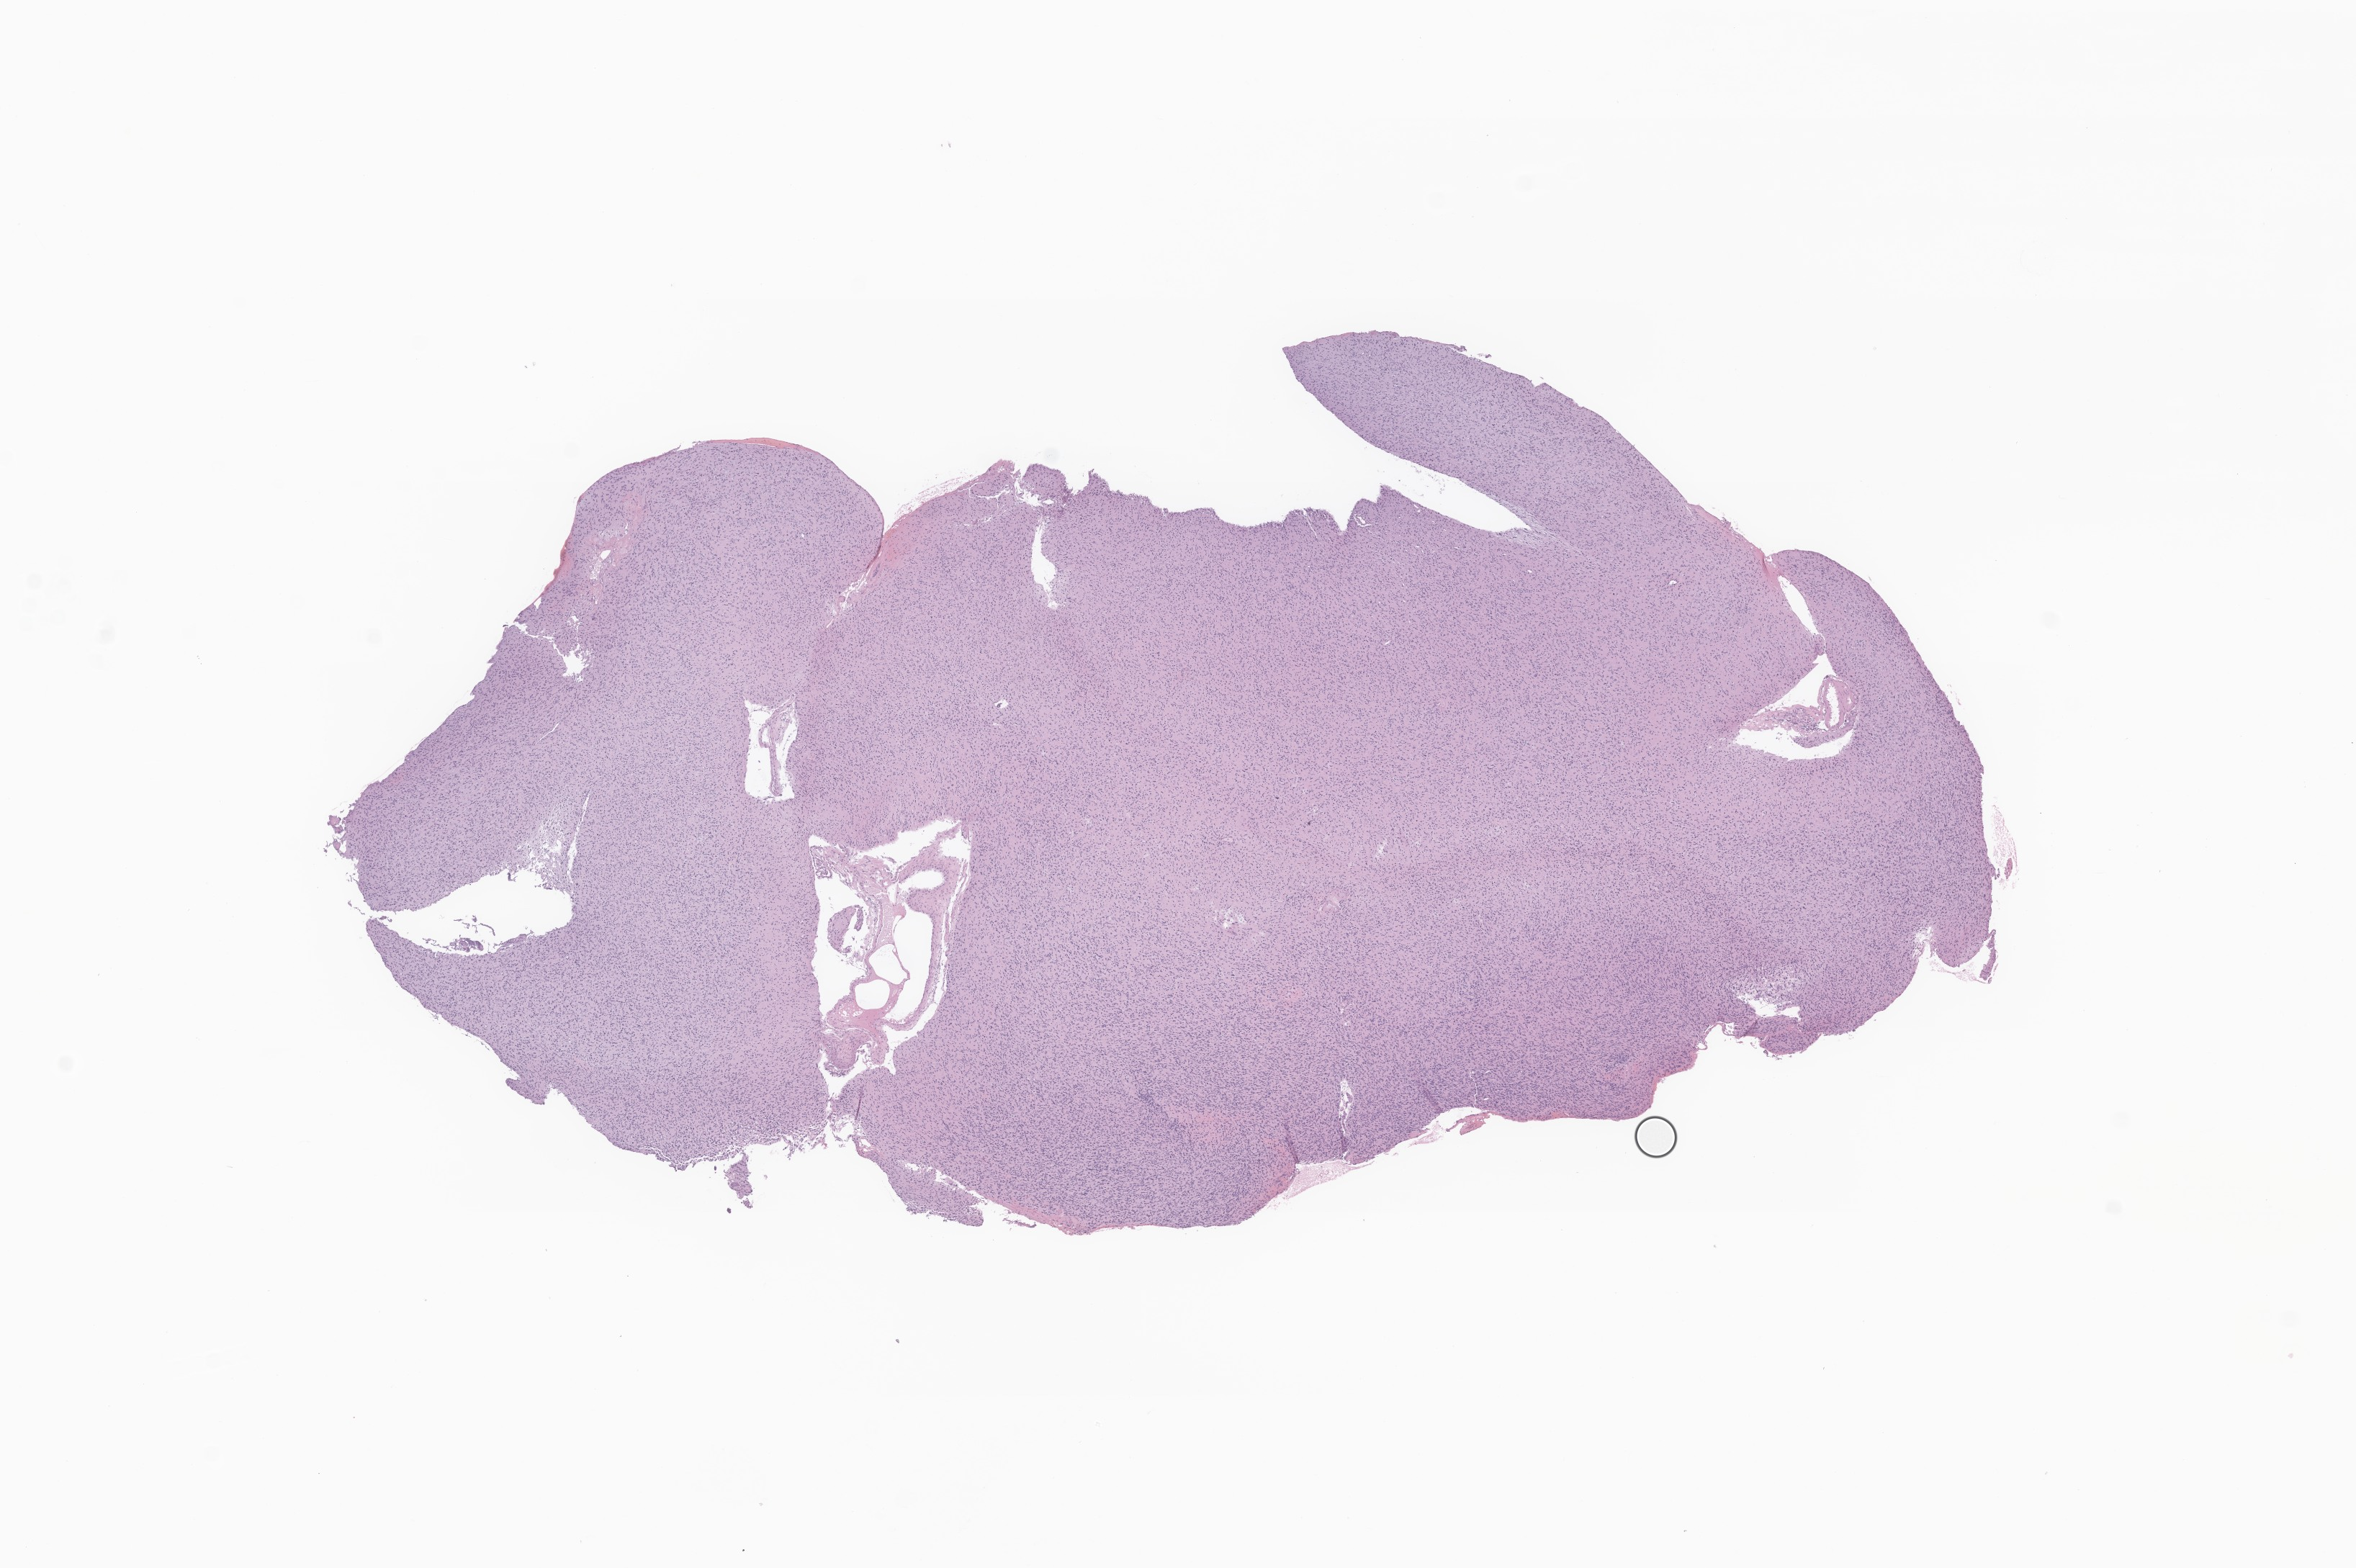
Haematoxylin and eosin whole-slide image of tumor tissue from the cerebrum, shown as a low-resolution overview of the whole scanned area (about 13.8 x 9.2 mm), formalin-fixed, paraffin-embedded (FFPE) tissue. Patient female; age 61 months (5 years 1 month).
* diagnosis: Glioblastoma, NOS